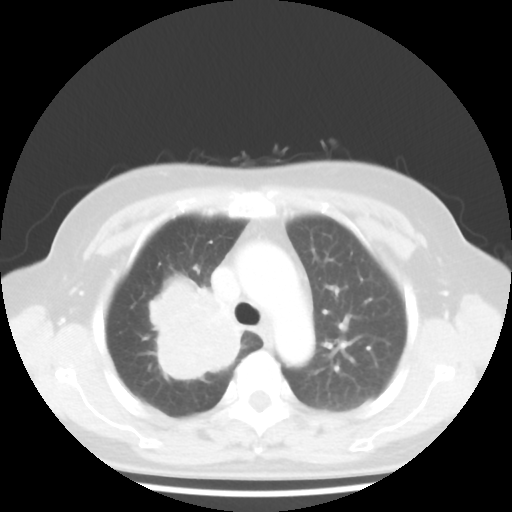
Chest CT, one axial slice. Position 32 of 44 along the scan axis. Lung window (W 1500 / L -600 HU). 512 × 512 image matrix. Female patient, age 62 years. From the clinical record (not read from this slice): clinical TNM (as recorded): T3 N0 M0.
Outlined on this slice (rectangle marked by the reading radiologist):
- lung tumour (recorded histology: small cell carcinoma): bounding box <137,275,258,390> (left, top, right, bottom; pixels)